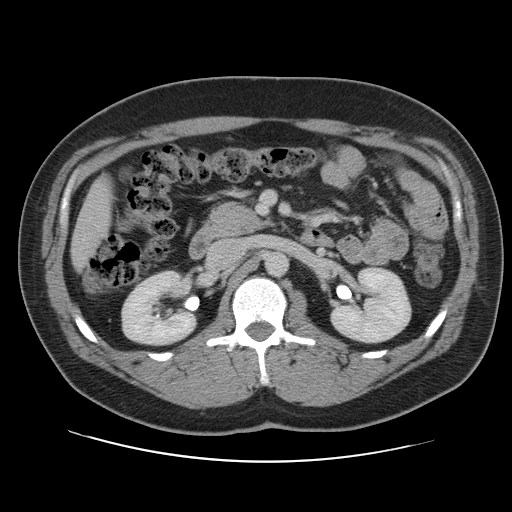
Contrast-enhanced abdominal CT, one axial slice. Slice 49 of 109 in the series (ordered by position). 120 kVp. Intravenous contrast given. Soft-tissue window (W 400 / L 40 HU). 512 × 512 image matrix. Male patient, age 35 years. Case-level facts recorded for this patient, not image findings: diagnosis: colorectal cancer liver metastases, imaged before liver resection; multiple liver metastases: yes; largest metastasis: 2.8 cm; chemotherapy before resection: yes.
Annotated regions visible in this slice (expert manual segmentation):
- liver: bounding box (x1, y1, x2, y2) in pixels: (73, 181, 111, 267)
- planned liver remnant (the part of the liver to remain after resection): (73, 179, 111, 267)